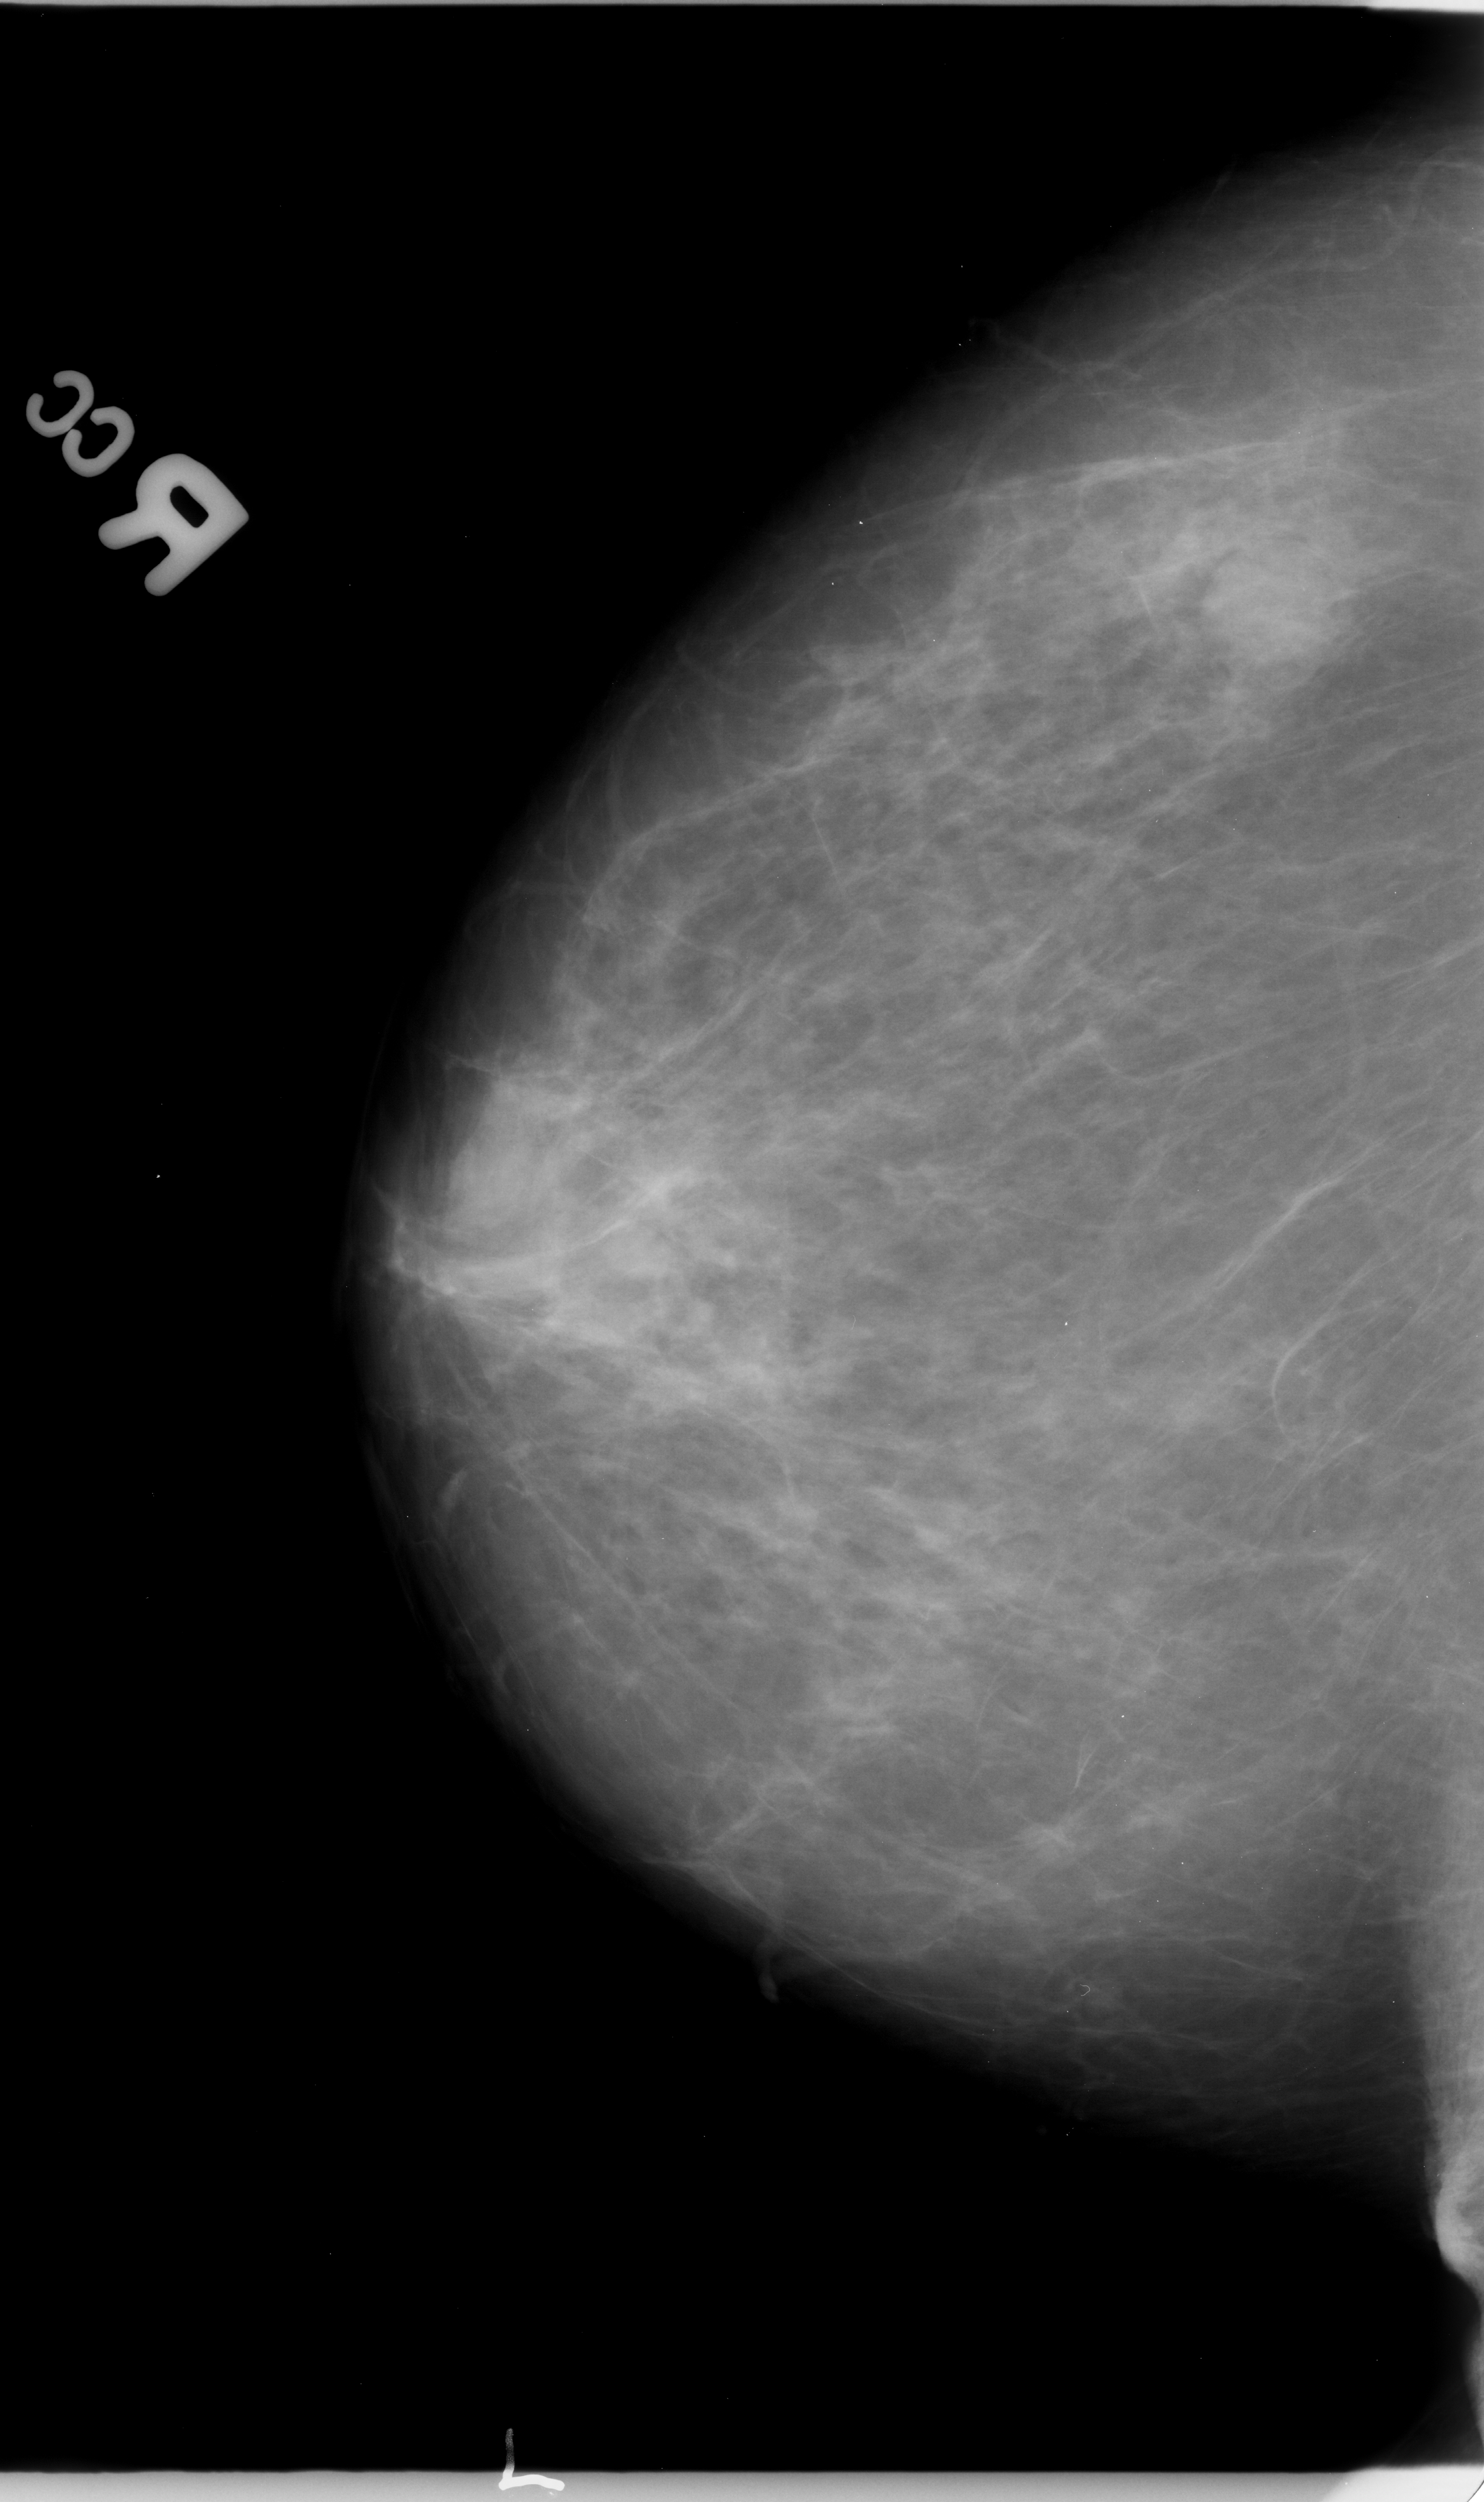
Scanned film-screen mammogram. Right breast. CC view. BI-RADS breast density category 3 (scale 1–4). 1484 × 2502 image matrix.
Expert-marked regions of interest on this film, with their recorded descriptors:
- mass, shape round, margins circumscribed; BI-RADS assessment category 3; pathology result (as recorded, not read from the image): benign: box from (x=1201, y=543) to (x=1357, y=672) px